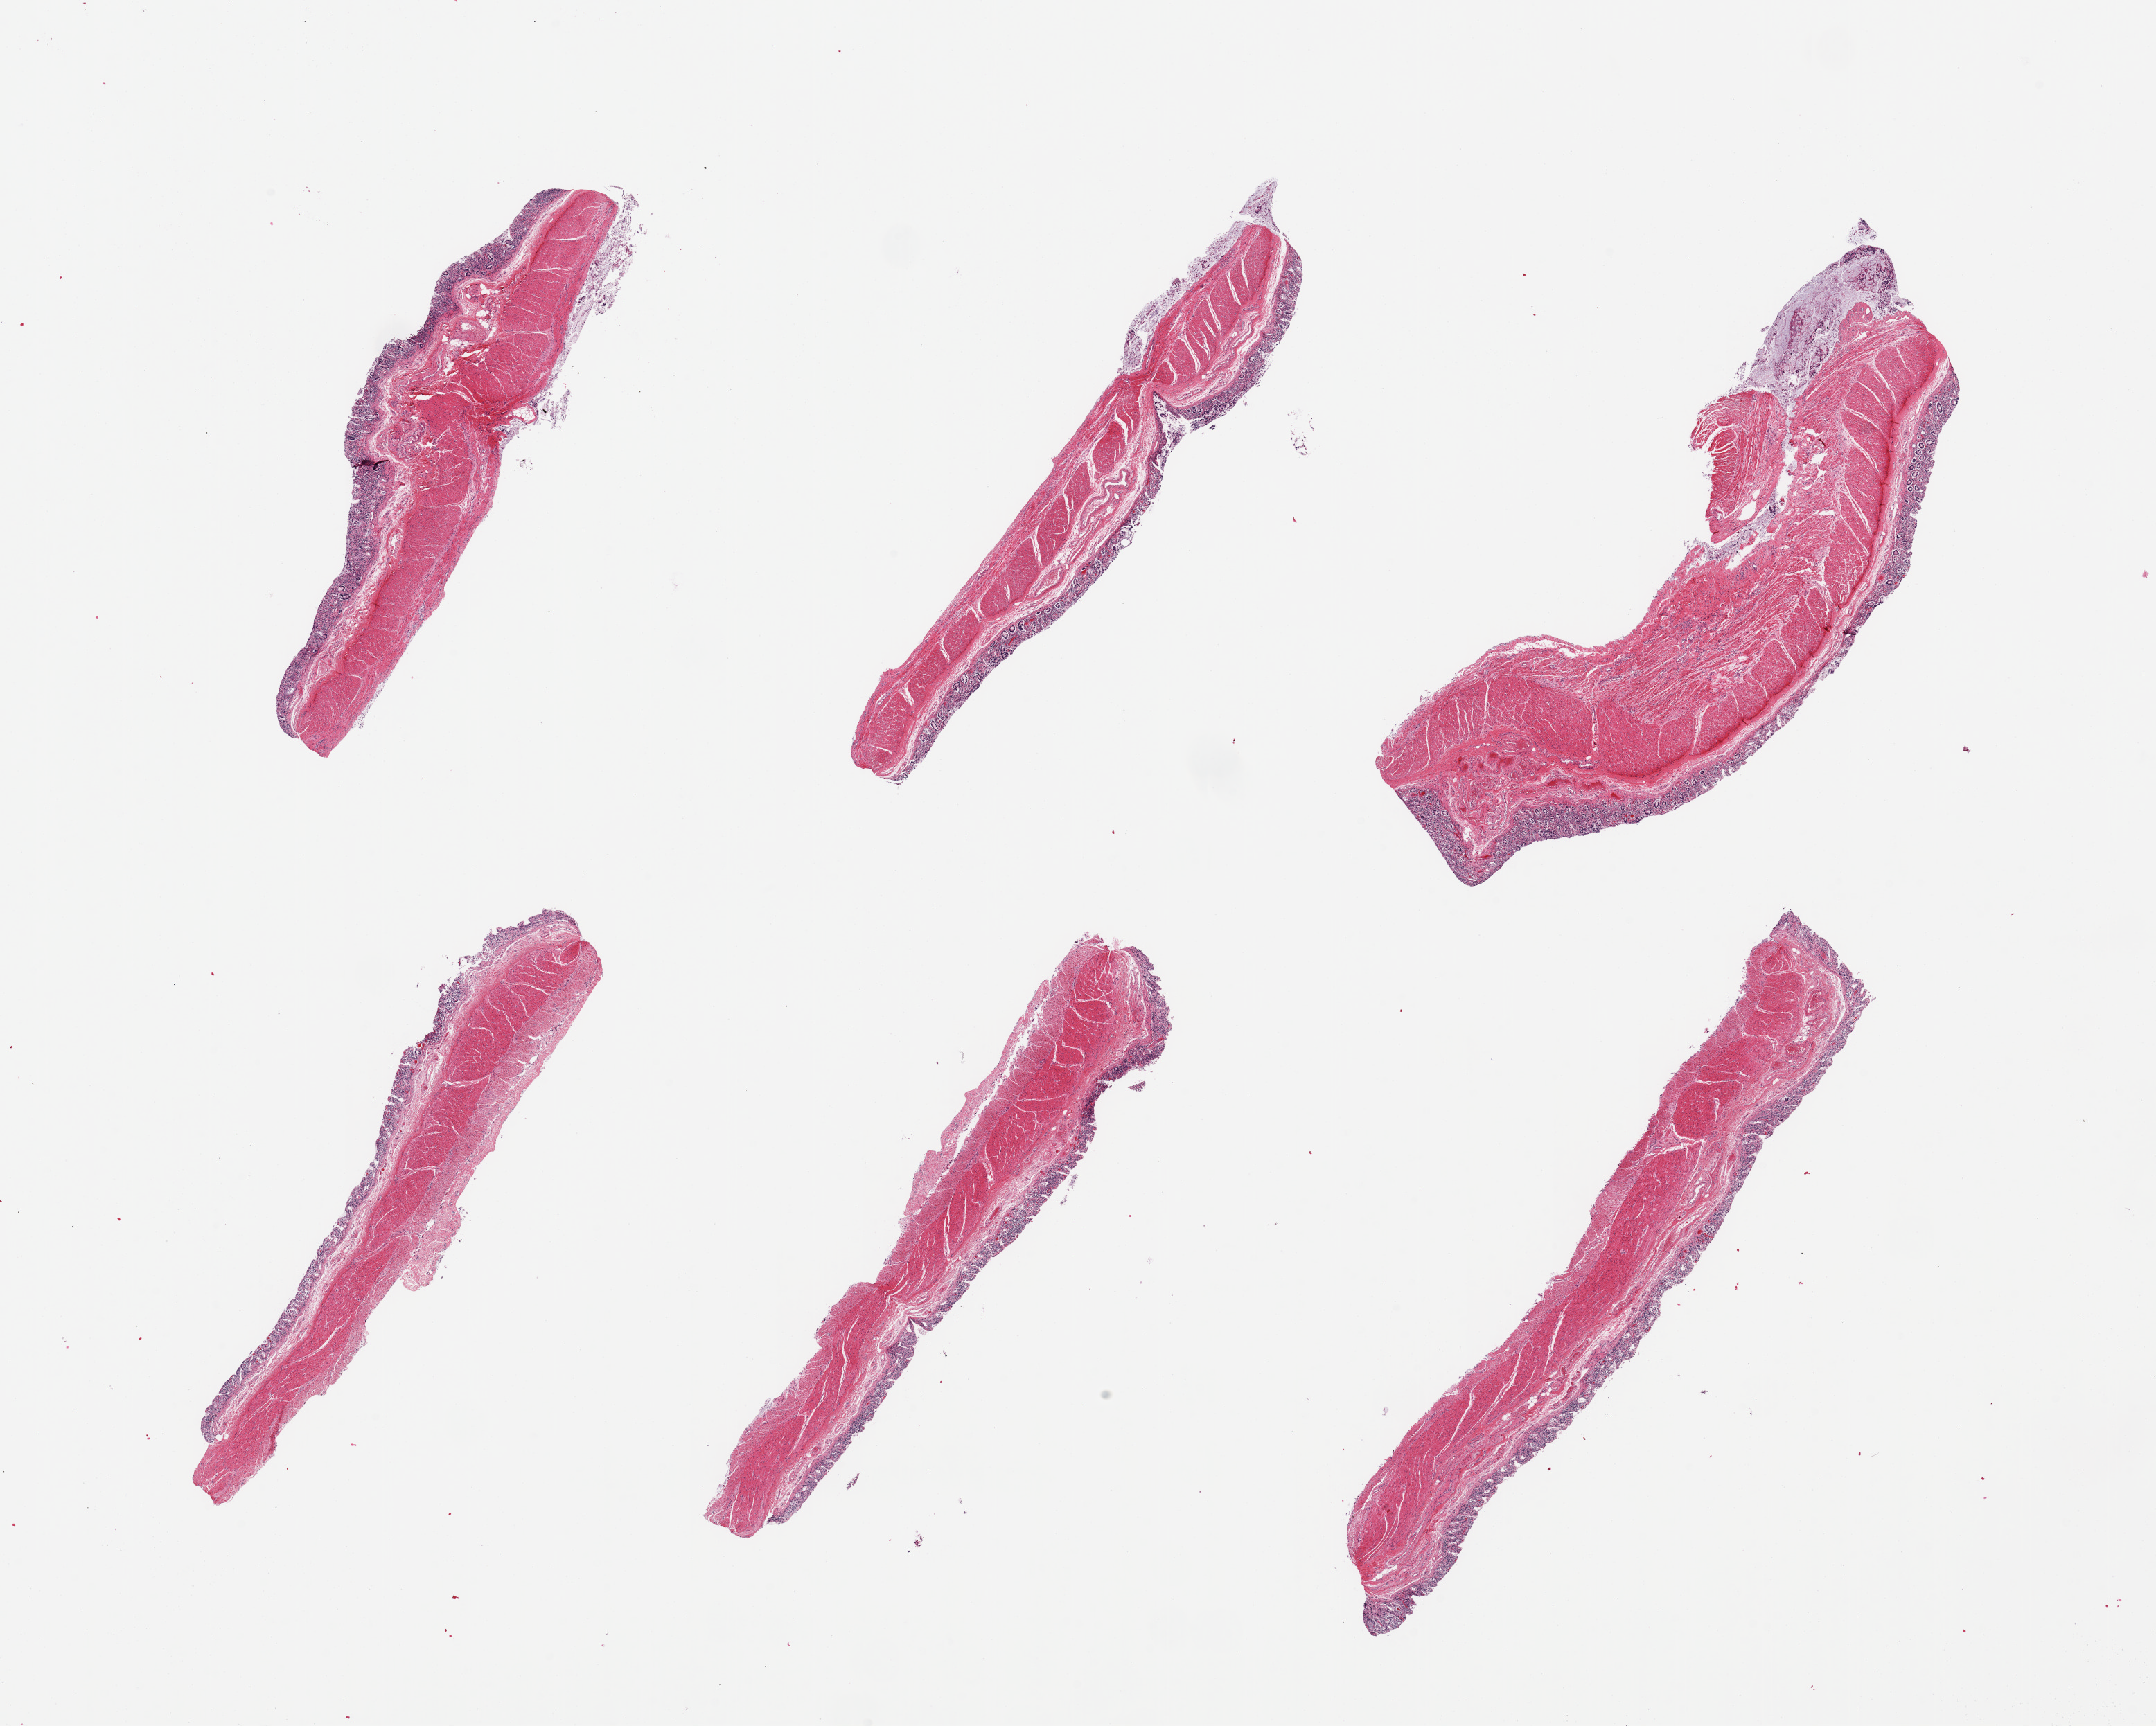
Whole-slide image, H&E stain, brightfield — low-resolution overview of the scanned area, about 24.6 x 19.7 mm, PAXgene-fixed, paraffin-embedded tissue, section of transverse colon (target tissue), donor tissue sample. Donor sex: female.
Pathologist's review note for this sample: 6 pieces; full thickness sections, mucosa largely autolyzed.